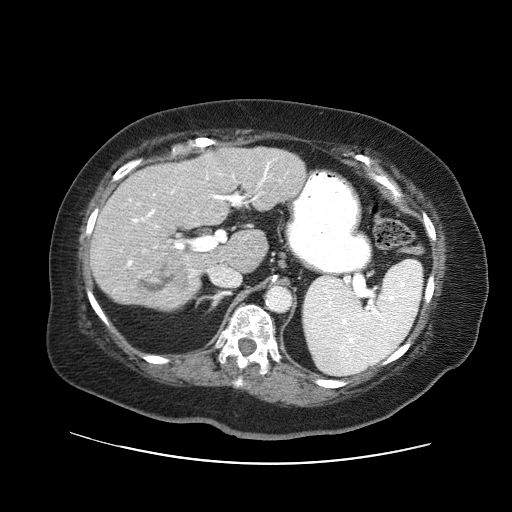
Contrast-enhanced abdominal CT (liver protocol), one axial slice; position 30 of 71 along the scan axis; 120 kVp; soft-tissue window (W 400 / L 40 HU); 2.5 mm slice thickness; 512 × 512 image matrix. From the clinical record (not read from this slice): diagnosis: hepatocellular carcinoma (patient treated with transarterial chemoembolisation; whether this scan precedes or follows treatment is not stated here); TNM stage (as recorded): Stage-II; Child-Pugh class: A; tumour differentiation: poorly differentiated; tumour nodularity: multinodular.
Structures marked on this image (semi-automatic segmentation, software-assisted and operator-edited):
- liver parenchyma outside the tumour (the mass and vessels are separate outlines, so this box may not span the whole liver): box from (x=90, y=146) to (x=306, y=310) px
- mass: (x=132, y=246)–(x=189, y=299)
- liver vessels: (x=120, y=159)–(x=276, y=277)